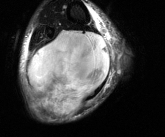
MRI of an extremity soft-tissue mass, one axial slice; slice 40 of 81 in the series (ordered by position); T2-weighted fat-saturated; MR volume resampled by the dataset authors to the PET/CT grid (not the native acquisition matrix); 165 × 137 image matrix, field of view 161 × 134 mm. Male patient. Case-level facts recorded for this patient, not image findings: histological type: liposarcoma - round cell; grade: high; site of the primary tumour: right calf.
Outlined on this slice (expert contour drawn on MRI and transferred to this co-registered scan by the dataset authors):
- gross tumour volume (mass): bounding box (x1, y1, x2, y2) in pixels: (28, 30, 111, 117)